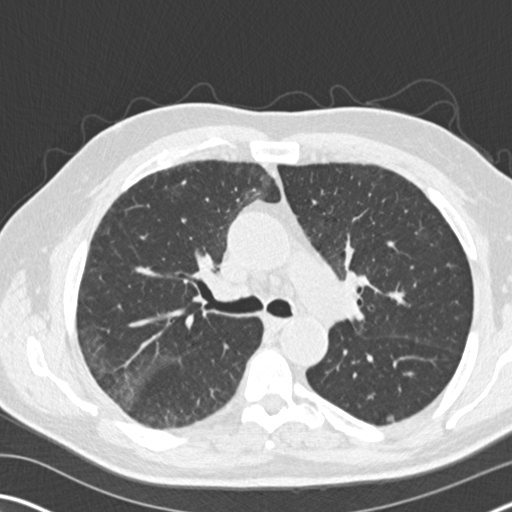
Low-dose screening chest CT, one axial slice. Position 108 of 169 along the scan axis. Reconstruction kernel B30f. Lung window (W 1500 / L -600 HU). 2 mm slice thickness. 512 × 512 image matrix.
Annotated regions visible in this slice (outlined manually by an expert reader):
- lesion 2 (nodule, lower lobe of left lung): bounding box (x1, y1, x2, y2) in pixels: (387, 416, 394, 421)